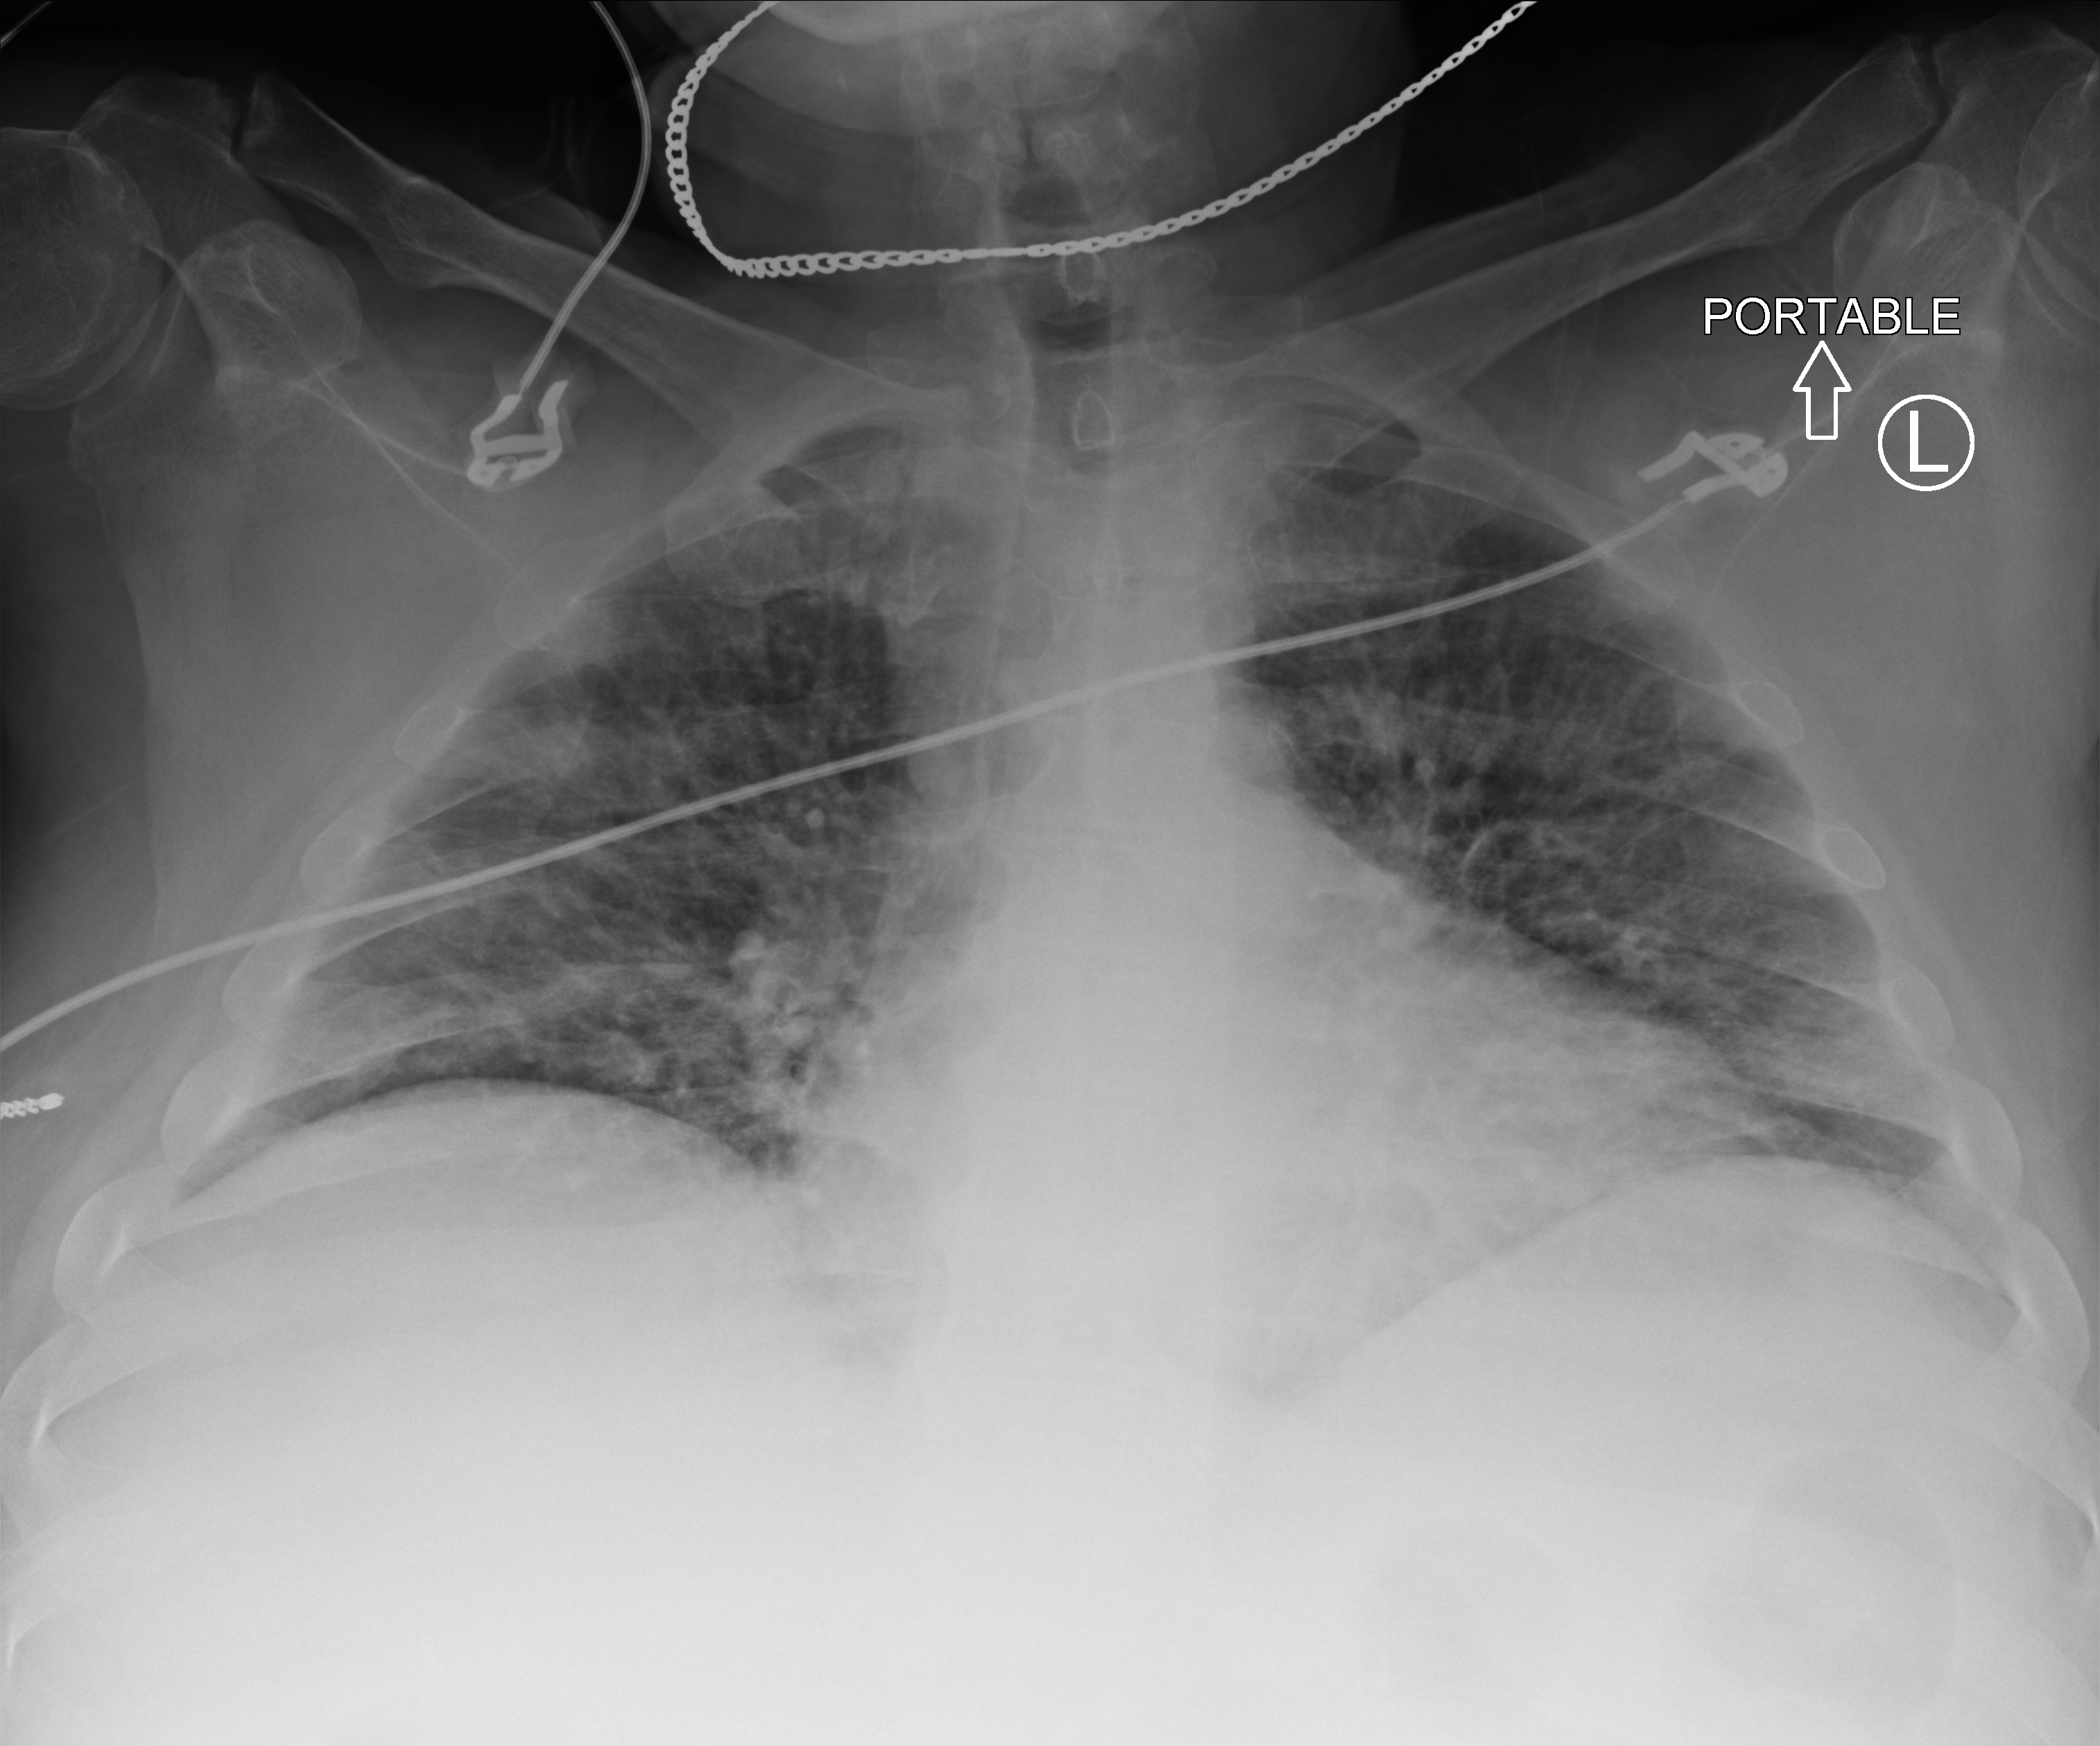
Bedside chest radiograph (computed radiography); anteroposterior (AP) projection. Patient hospitalised with COVID-19; male, aged 18–59 years.
From the hospital-stay record, not from the radiograph (when in the stay this image was taken is not recorded):
- admitted to intensive care during this hospital stay: no